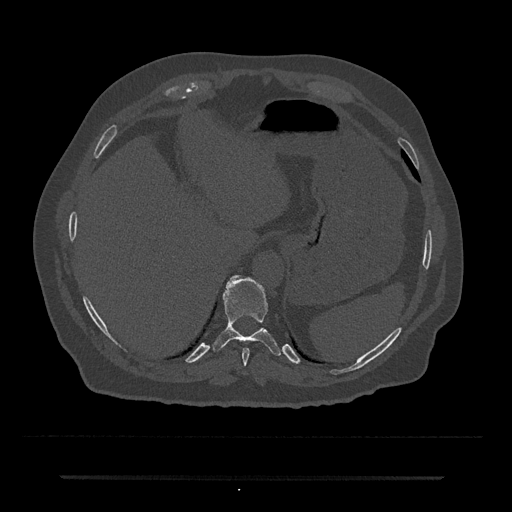
CT including the spine, one axial slice. Position 236 of 797 along the scan axis. 120 kVp. Bone window (W 1800 / L 400 HU). 0.5 mm slice thickness. 512 × 512 image matrix, field of view 437 × 437 mm. Patient: male, 69 years. From the clinical record (not read from this slice): primary cancer: prostate.
Annotated regions visible in this slice (semi-automatically segmented with operator editing):
- T10 vertebra: box from (x=212, y=275) to (x=281, y=356) px
- T9 vertebra: (x=242, y=348)–(x=250, y=366)